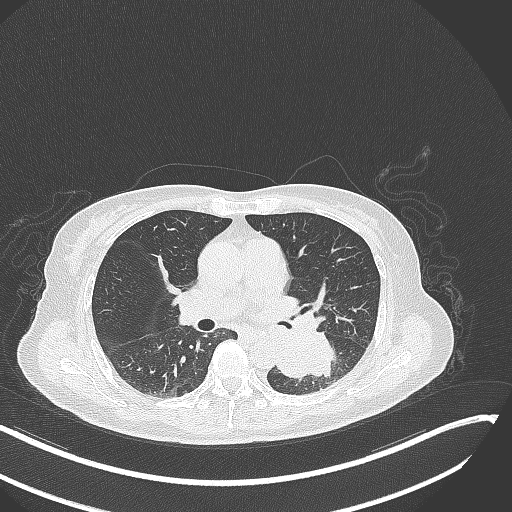
Chest CT, one axial slice. Lung window (W 1500 / L -600 HU). 512 × 512 image matrix. Female patient, age 64 years. Case-level facts recorded for this patient, not image findings: clinical TNM (as recorded): T3 N1 M1; histopathological grade: G3.
Annotated regions visible in this slice (bounding box drawn by a radiologist):
- lung tumour (recorded histology: small cell carcinoma): bounding box <276,325,336,380> (left, top, right, bottom; pixels)